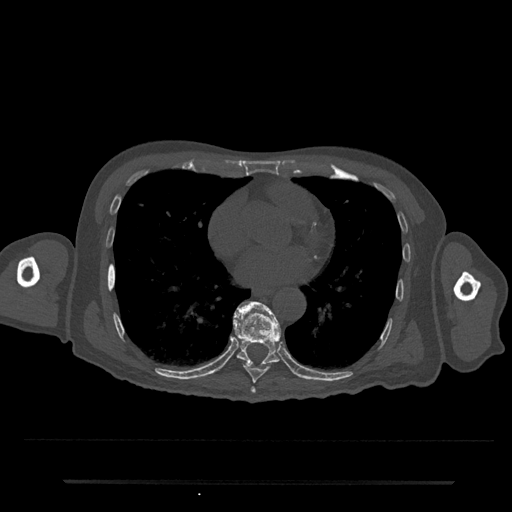
CT including the spine, one axial slice. Slice 396 of 797 in the series (ordered by position). Reconstruction kernel Br40s/3. 120 kVp. Bone window (W 1800 / L 400 HU). 0.5 mm slice thickness. 512 × 512 image matrix, field of view 427 × 427 mm. Male patient, age 74 years. From the clinical record (not read from this slice): primary cancer: prostate.
Outlined on this slice (semi-automatic segmentation, software-assisted and operator-edited):
- T7 vertebra: bounding box (x1, y1, x2, y2) in pixels: (250, 387, 256, 394)
- T8 vertebra: (243, 362, 270, 383)
- T9 vertebra: (233, 301, 282, 364)